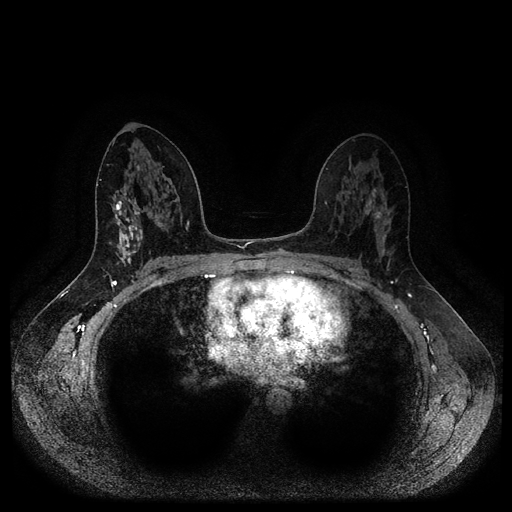
Breast MRI (dynamic contrast-enhanced, multi-phase), one axial slice. Position 57 of 116 along the scan axis. Dynamic contrast-enhanced series, time point 2 of 5 at this slice position (early post-contrast). 1.5 T. TE 2.6 ms, TR 5.3 ms. 2 mm slice thickness. 512 × 512 image matrix, field of view 360 × 360 mm. Patient: female, 45 years.
Annotated regions visible in this slice (semi-automatically segmented with operator editing):
- breast lesion (labelled benign in the annotation): bounding box (x1, y1, x2, y2) in pixels: (111, 195, 143, 267)